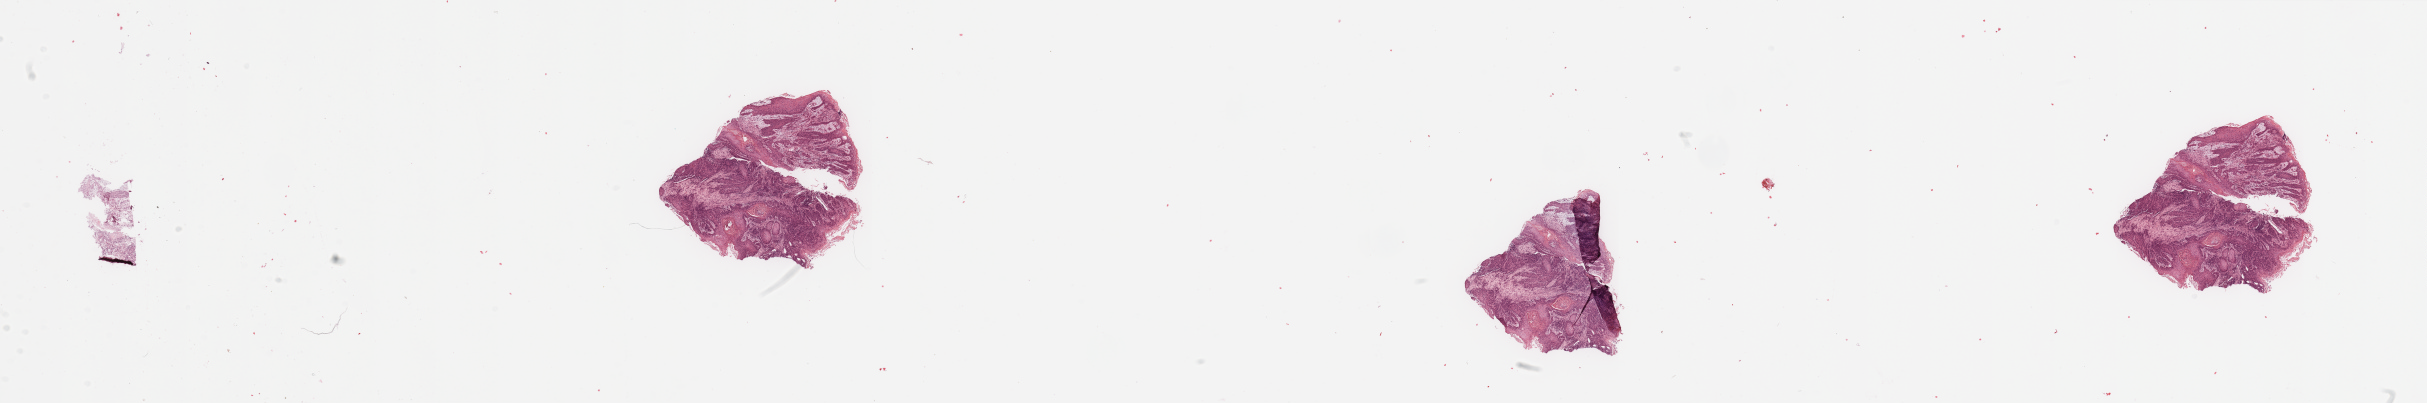
Digitized Hematoxylin and eosin (H&E) stained tissue section (whole slide), shown as a low-resolution overview of the whole scanned area (about 38.4 x 6.4 mm). Tumour tissue sample, sampled site: larynx. Male, 61 y/o. Histologic grade: G1 (well differentiated). Slide review estimates, as recorded: tumour nuclei 85%, necrosis 5%.
AJCC pathologic stage: II. Primary tumour site (as recorded): larynx. Histologic diagnosis: Squamous cell carcinoma, NOS (larynx, NOS).